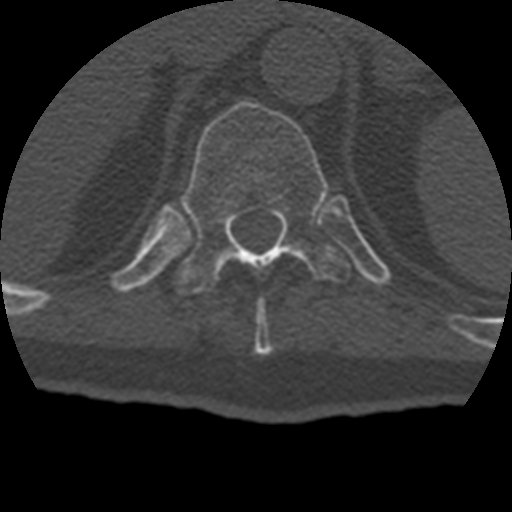
CT including the spine, one axial slice; slice 202 of 399 in the series (ordered by position); 120 kVp; bone window (W 1800 / L 400 HU); 1.25 mm slice thickness; 512 × 512 image matrix, field of view 160 × 160 mm. Patient age 69 years. Case-level facts recorded for this patient, not image findings: primary cancer: prostate.
Outlined on this slice (semi-automatically segmented with operator editing):
- T10 vertebra: bounding box (x1, y1, x2, y2) in pixels: (254, 299, 272, 354)
- T11 vertebra: (177, 101, 351, 295)